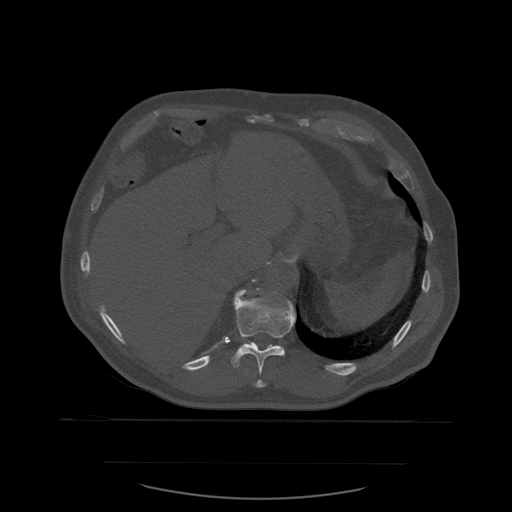
CT including the spine, one axial slice. Position 293 of 590 along the scan axis. Bone window (W 1800 / L 400 HU). 1.25 mm slice thickness. 512 × 512 image matrix. Patient age 71 years. Case-level facts recorded for this patient, not image findings: primary cancer: lung.
Outlined on this slice (semi-automatic segmentation, software-assisted and operator-edited):
- T11 vertebra: bounding box [x1, y1, x2, y2] px = [231, 290, 297, 388]
- T12 vertebra: [235, 288, 281, 344]